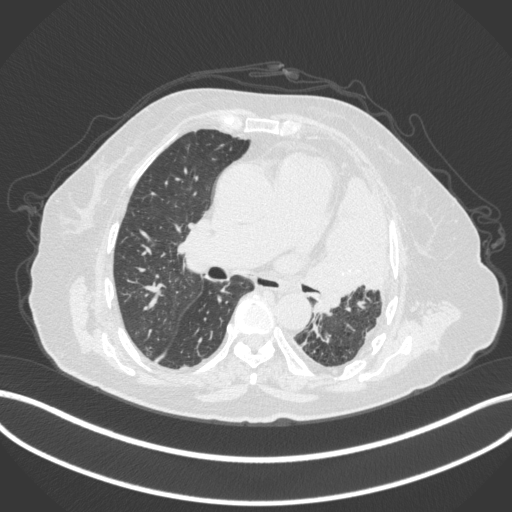
Chest CT, one axial slice. Position 211 of 399 along the scan axis. Lung window (W 1500 / L -600 HU). 1 mm slice thickness. 512 × 512 image matrix, field of view 400 × 400 mm. Female patient, age 75 years. From the clinical record (not read from this slice): clinical TNM (as recorded): T3 N3 M1.
Structures marked on this image (rectangle marked by the reading radiologist):
- lung tumour (recorded histology: adenocarcinoma): bounding box [x1, y1, x2, y2] px = [298, 171, 390, 318]